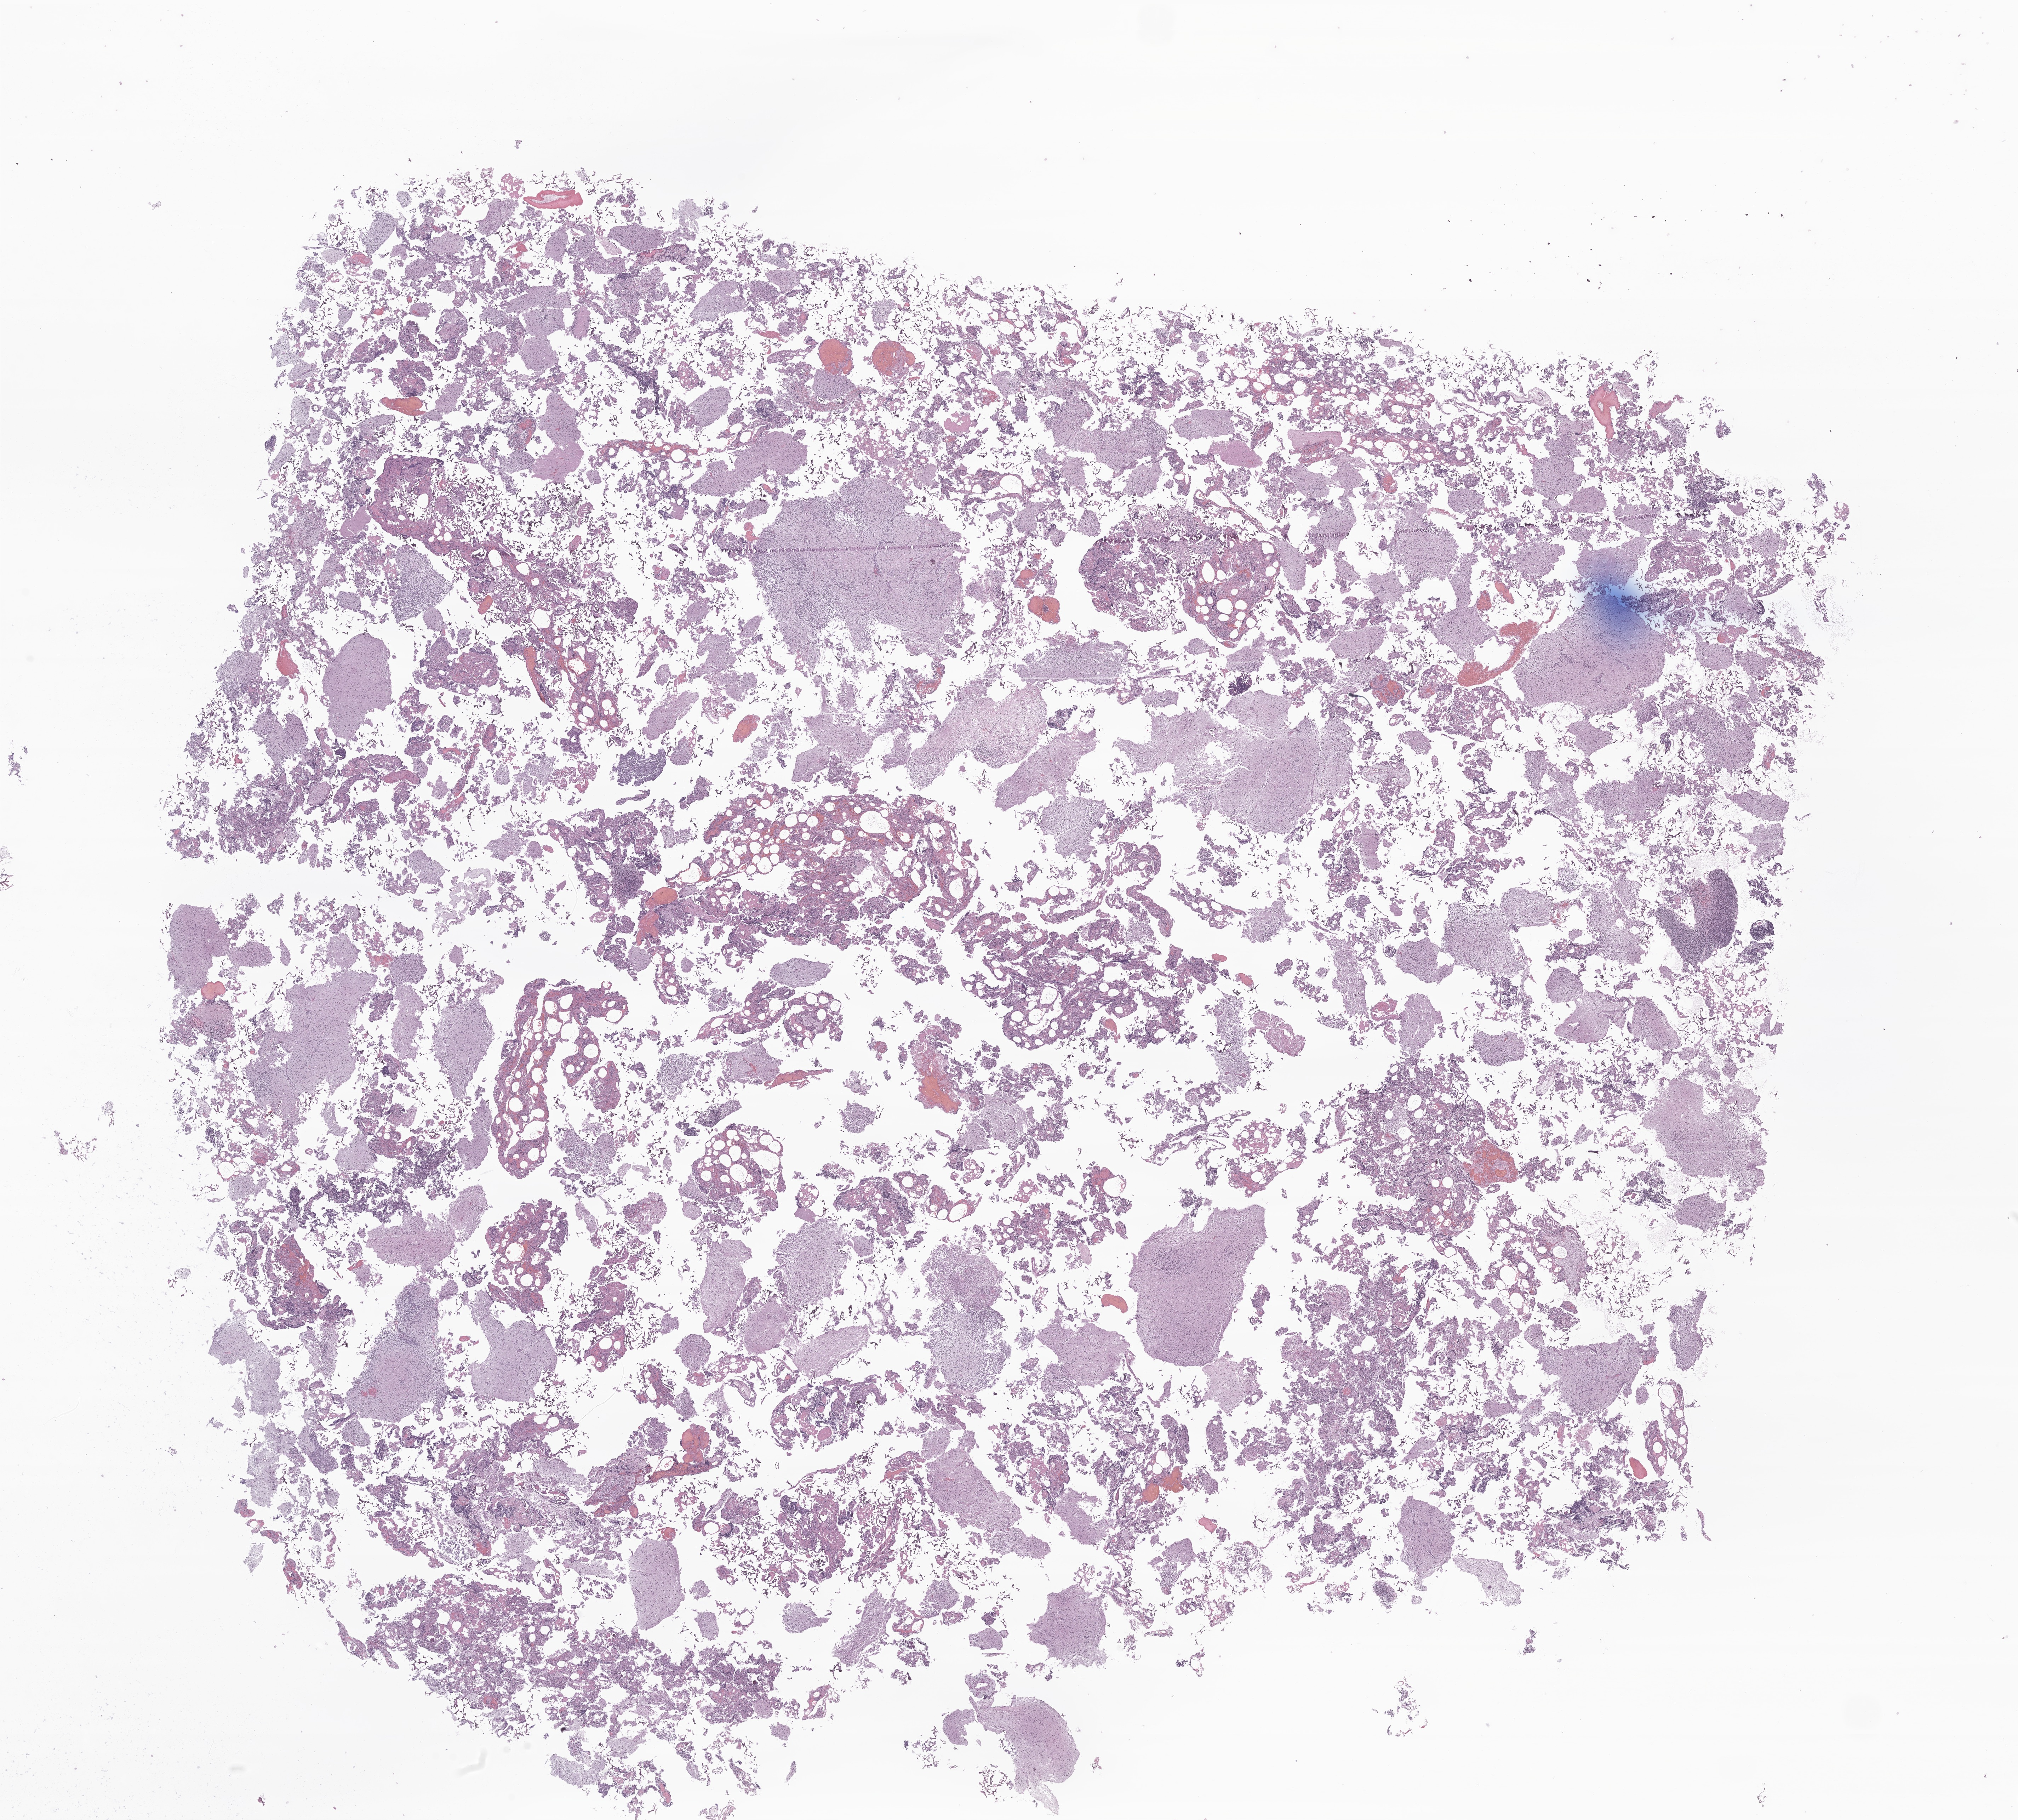
Hematoxylin and eosin (H&E) whole-slide image of tumor tissue from the cerebellum — shown as a low-resolution overview of the whole scanned area (about 24.0 x 21.7 mm). Formalin-fixed paraffin-embedded section. Patient male; age 683 days (about 1.9 years).
Recorded diagnosis: Atypical teratoid/rhabdoid tumor.